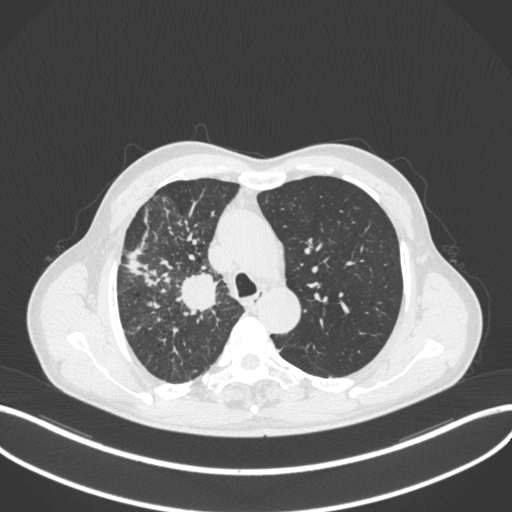
Chest CT, one axial slice. 120 kVp. Lung window (W 1500 / L -600 HU). 1 mm slice thickness. 512 × 512 image matrix. Male patient, age 69 years. From the clinical record (not read from this slice): clinical TNM (as recorded): T2a N0 M0.
Outlined on this slice (rectangle marked by the reading radiologist):
- lung tumour (recorded histology: adenocarcinoma): bounding box (x1, y1, x2, y2) in pixels: (176, 272, 223, 312)